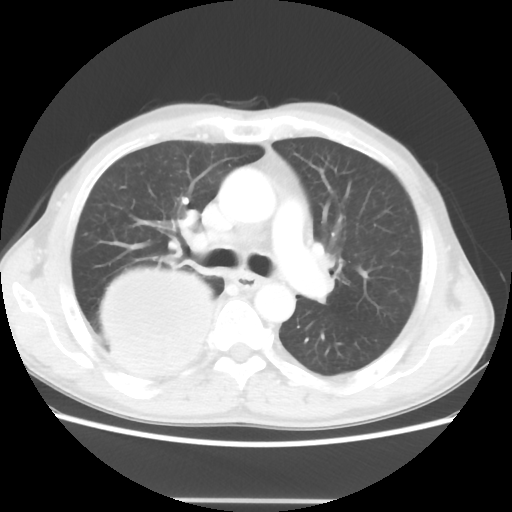
Chest CT, one axial slice; position 30 of 48 along the scan axis; 100 kVp; lung window (W 1500 / L -600 HU); 5 mm slice thickness; 512 × 512 image matrix, field of view 361 × 361 mm. Patient: male, 66 years. Case-level facts recorded for this patient, not image findings: clinical TNM (as recorded): T4 N1 M1; histopathological grade: G3.
Annotated regions visible in this slice (rectangle marked by the reading radiologist):
- lung tumour (recorded histology: small cell carcinoma): box from (x=91, y=262) to (x=221, y=383) px